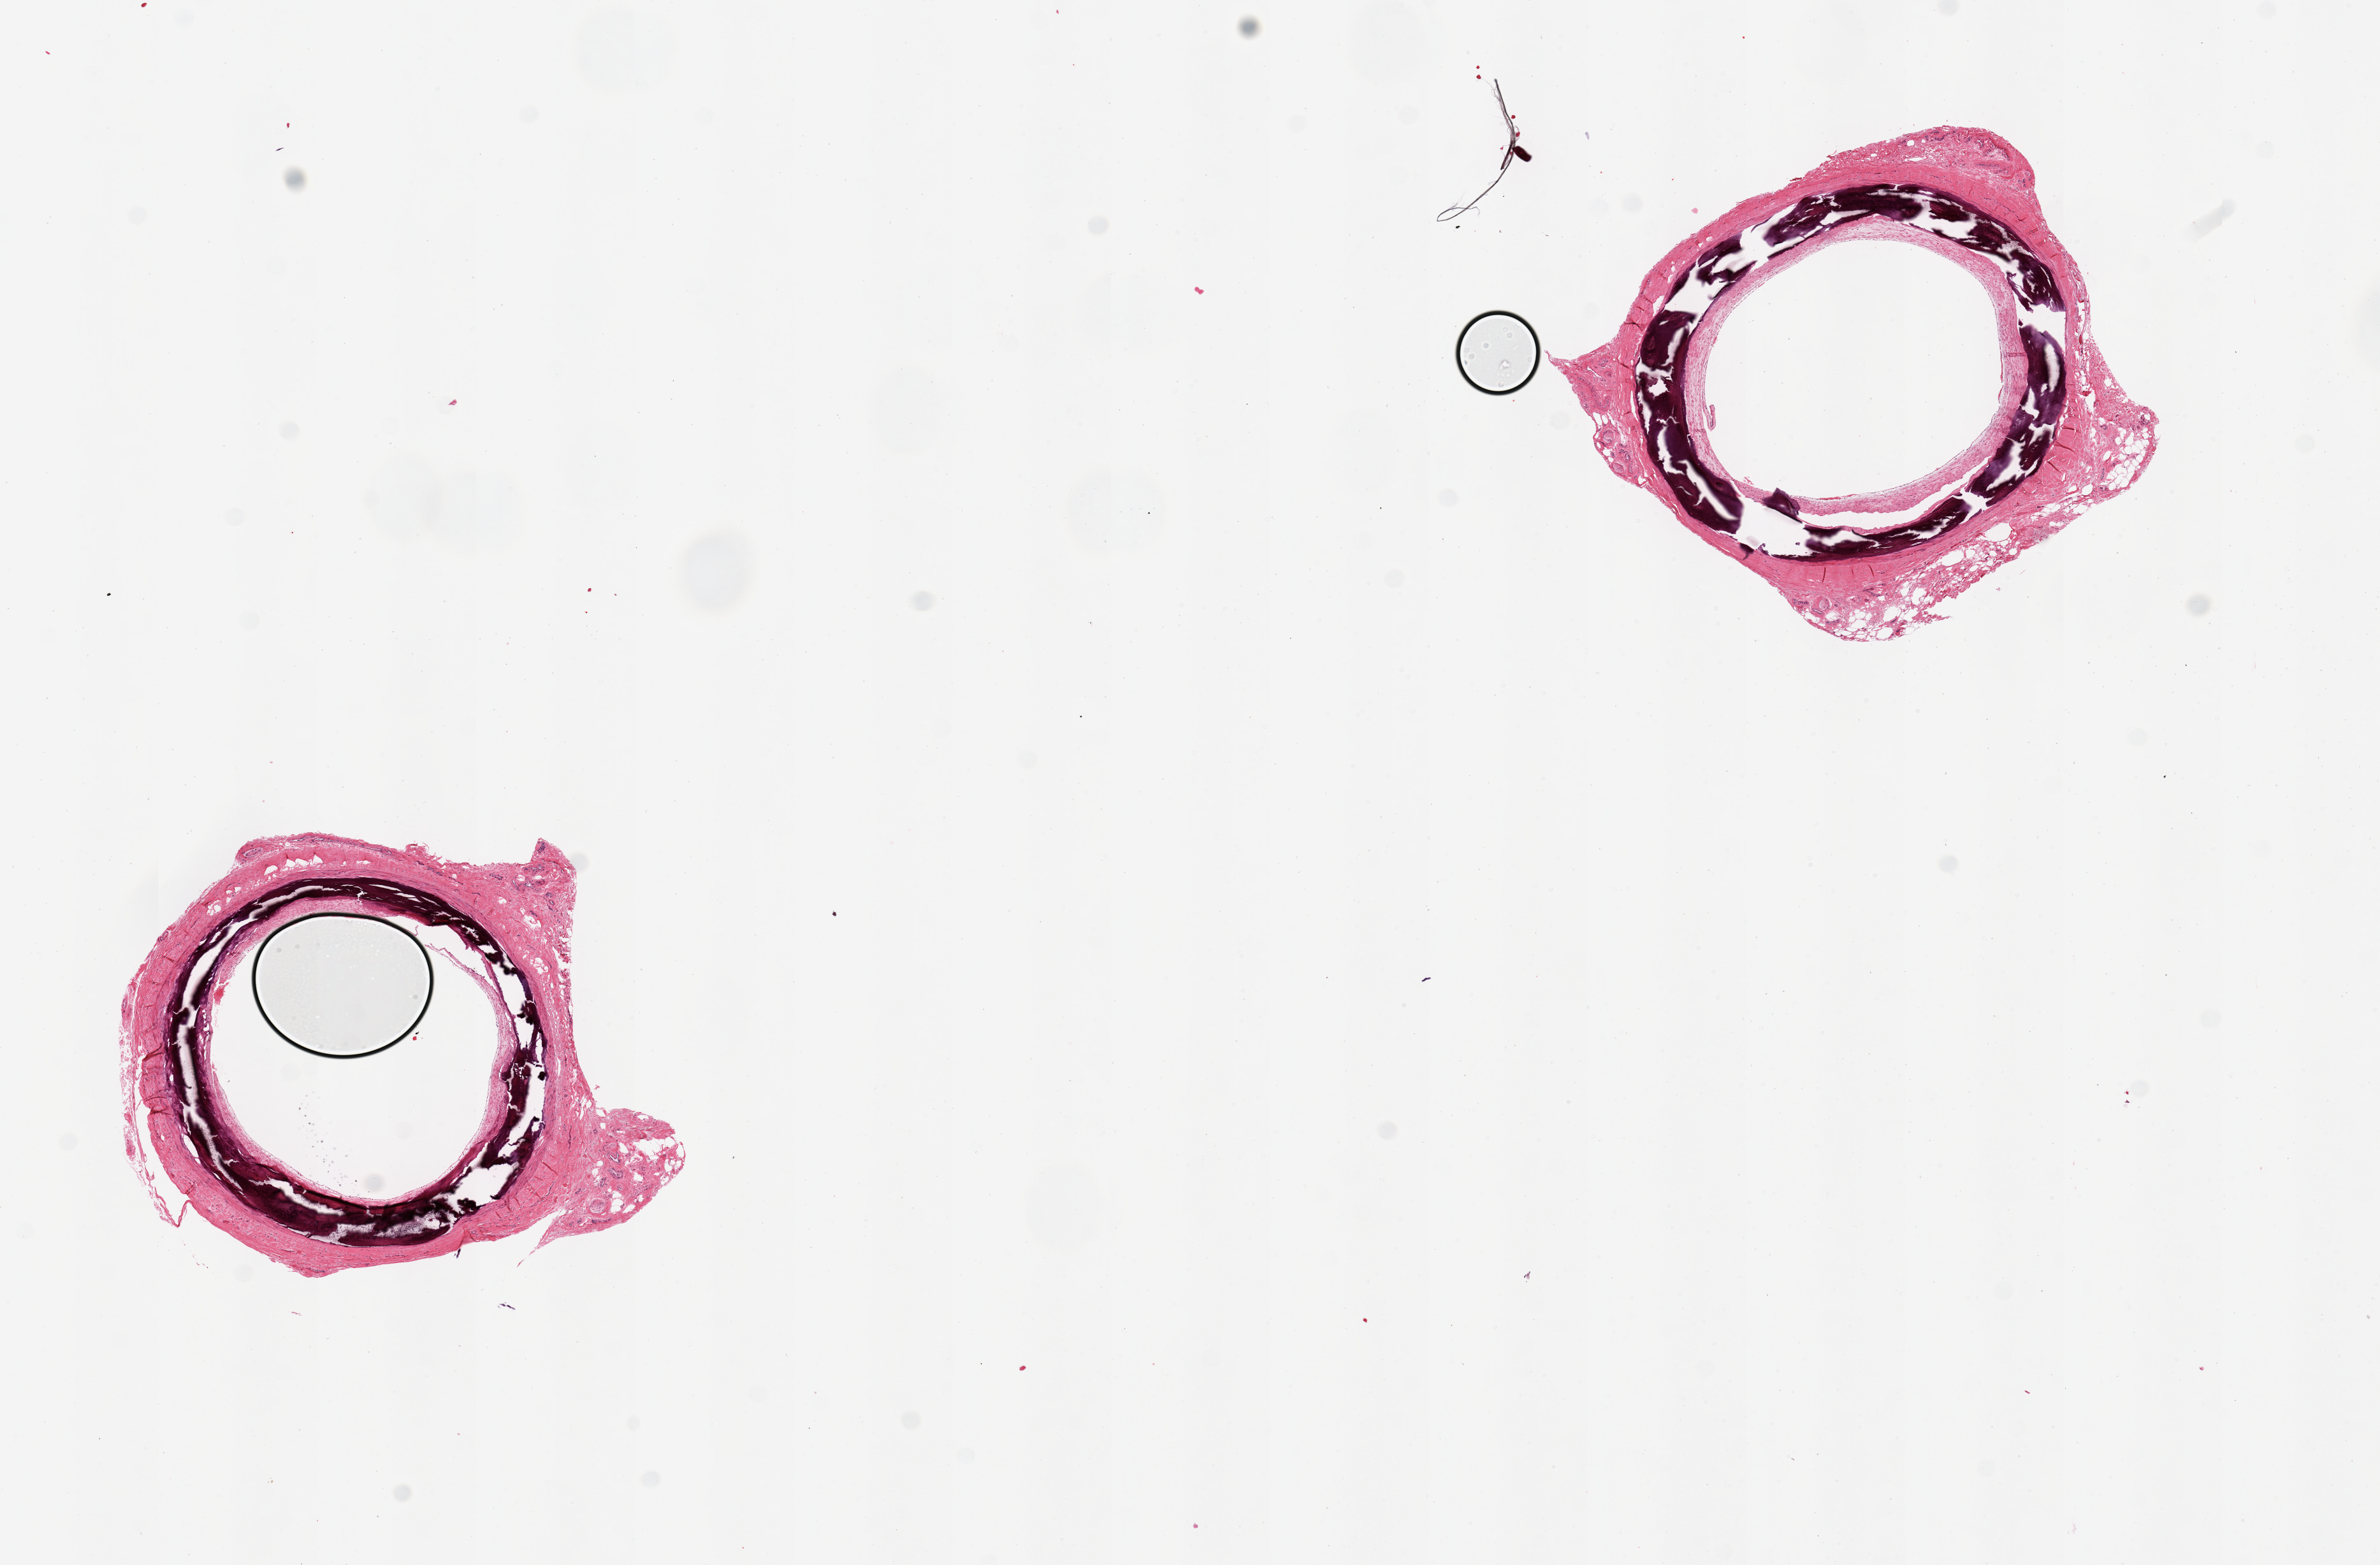
Hematoxylin and eosin (H&E) whole-slide image, a low-resolution overview of the entire scanned area, about 14.8 x 9.7 mm; PAXgene-fixed paraffin-embedded (PFPE) section; target tissue: tibial artery; tissue donor sample. Donor sex: male.
Review note (as recorded): 2 pieces, pronounced circumferential Monckeberg's medial sclerosis.